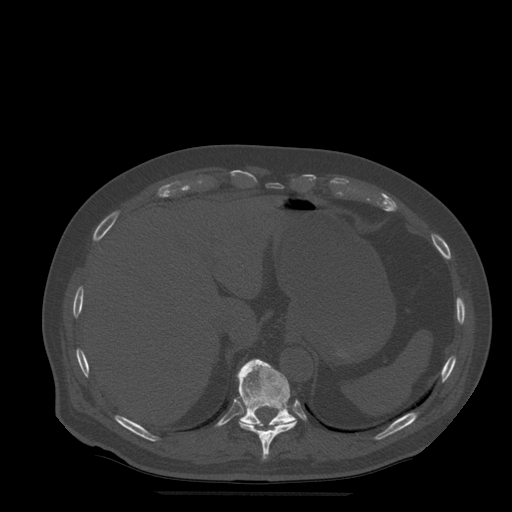
CT including the spine, one axial slice; slice 257 of 522 in the series (ordered by position); bone window (W 1800 / L 400 HU); 512 × 512 image matrix. Patient age 72 years. Case-level facts recorded for this patient, not image findings: primary cancer: prostate.
Structures marked on this image (semi-automatic segmentation, software-assisted and operator-edited):
- T10 vertebra: bounding box (x1, y1, x2, y2) in pixels: (239, 420, 297, 460)
- T11 vertebra: (237, 359, 297, 427)